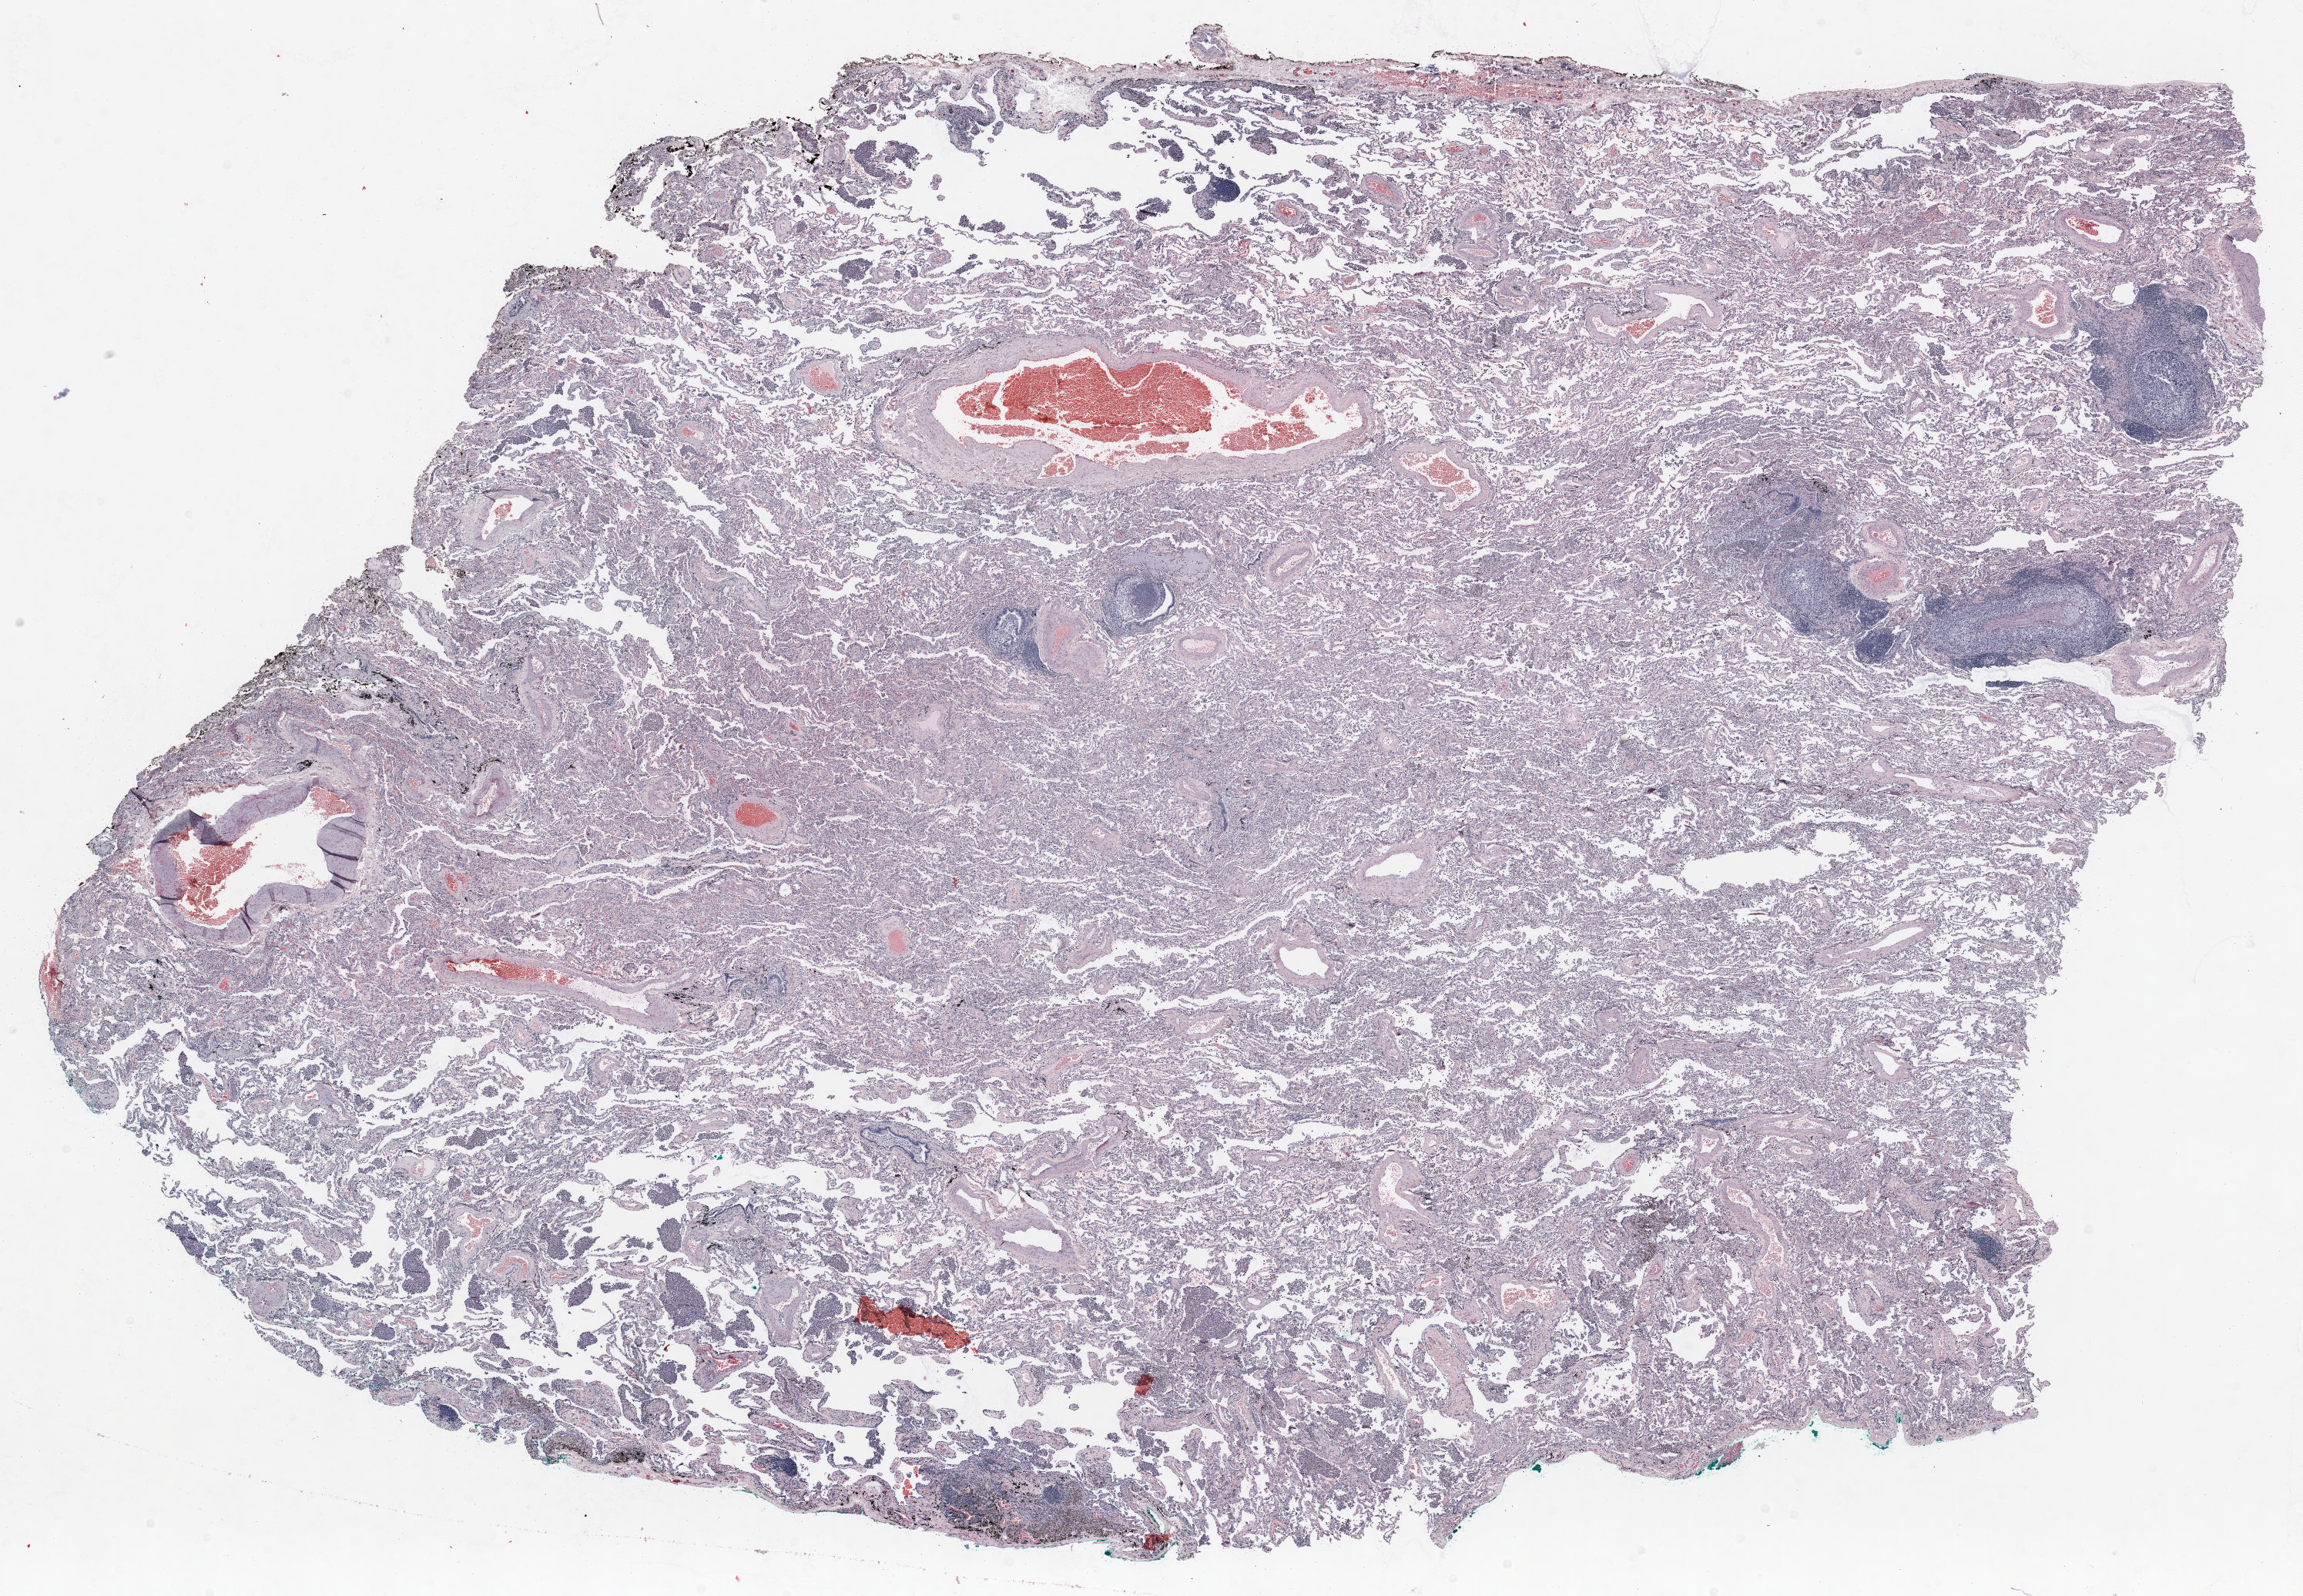
Whole-slide histology image, Hematoxylin and eosin (H&E) stained, shown as a low-resolution overview of the whole scanned area (about 24.0 x 16.6 mm), formalin-fixed paraffin-embedded (FFPE) section, lung. Male, age 58 at enrolment. Current smoker at enrolment.
Participant's lung-cancer diagnosis: Squamous cell carcinoma, NOS (ICD-O-3 8070/3).